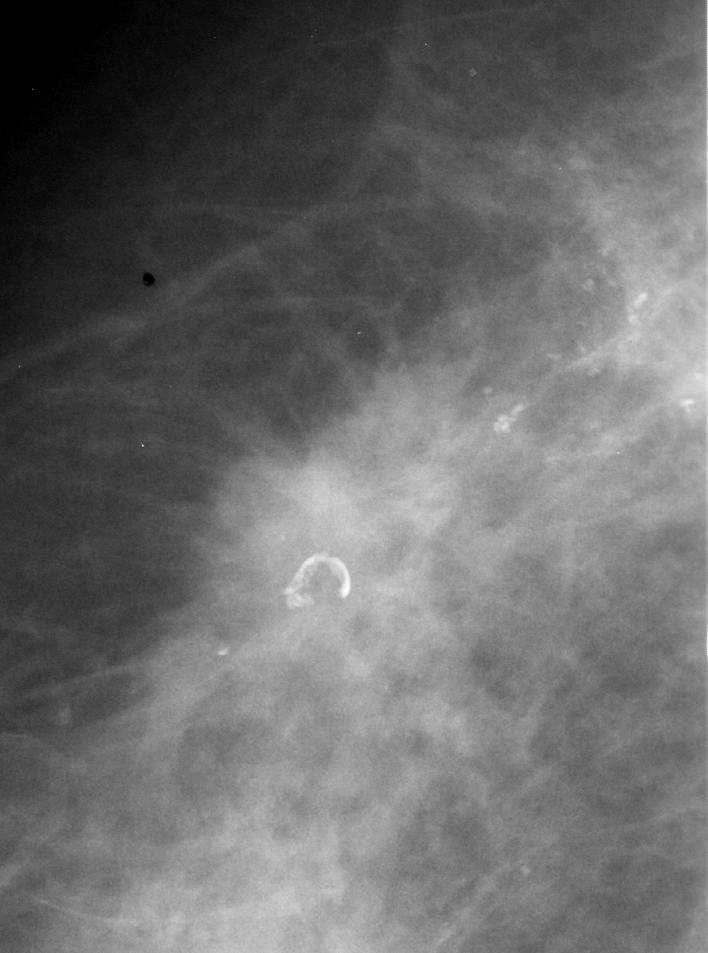
Region of interest cut from a scanned film mammogram (one marked finding), right breast, CC view.
- Finding: calcifications, morphology pleomorphic, distribution segmental; BI-RADS assessment category 5; pathology result (as recorded, not read from the image): malignant.